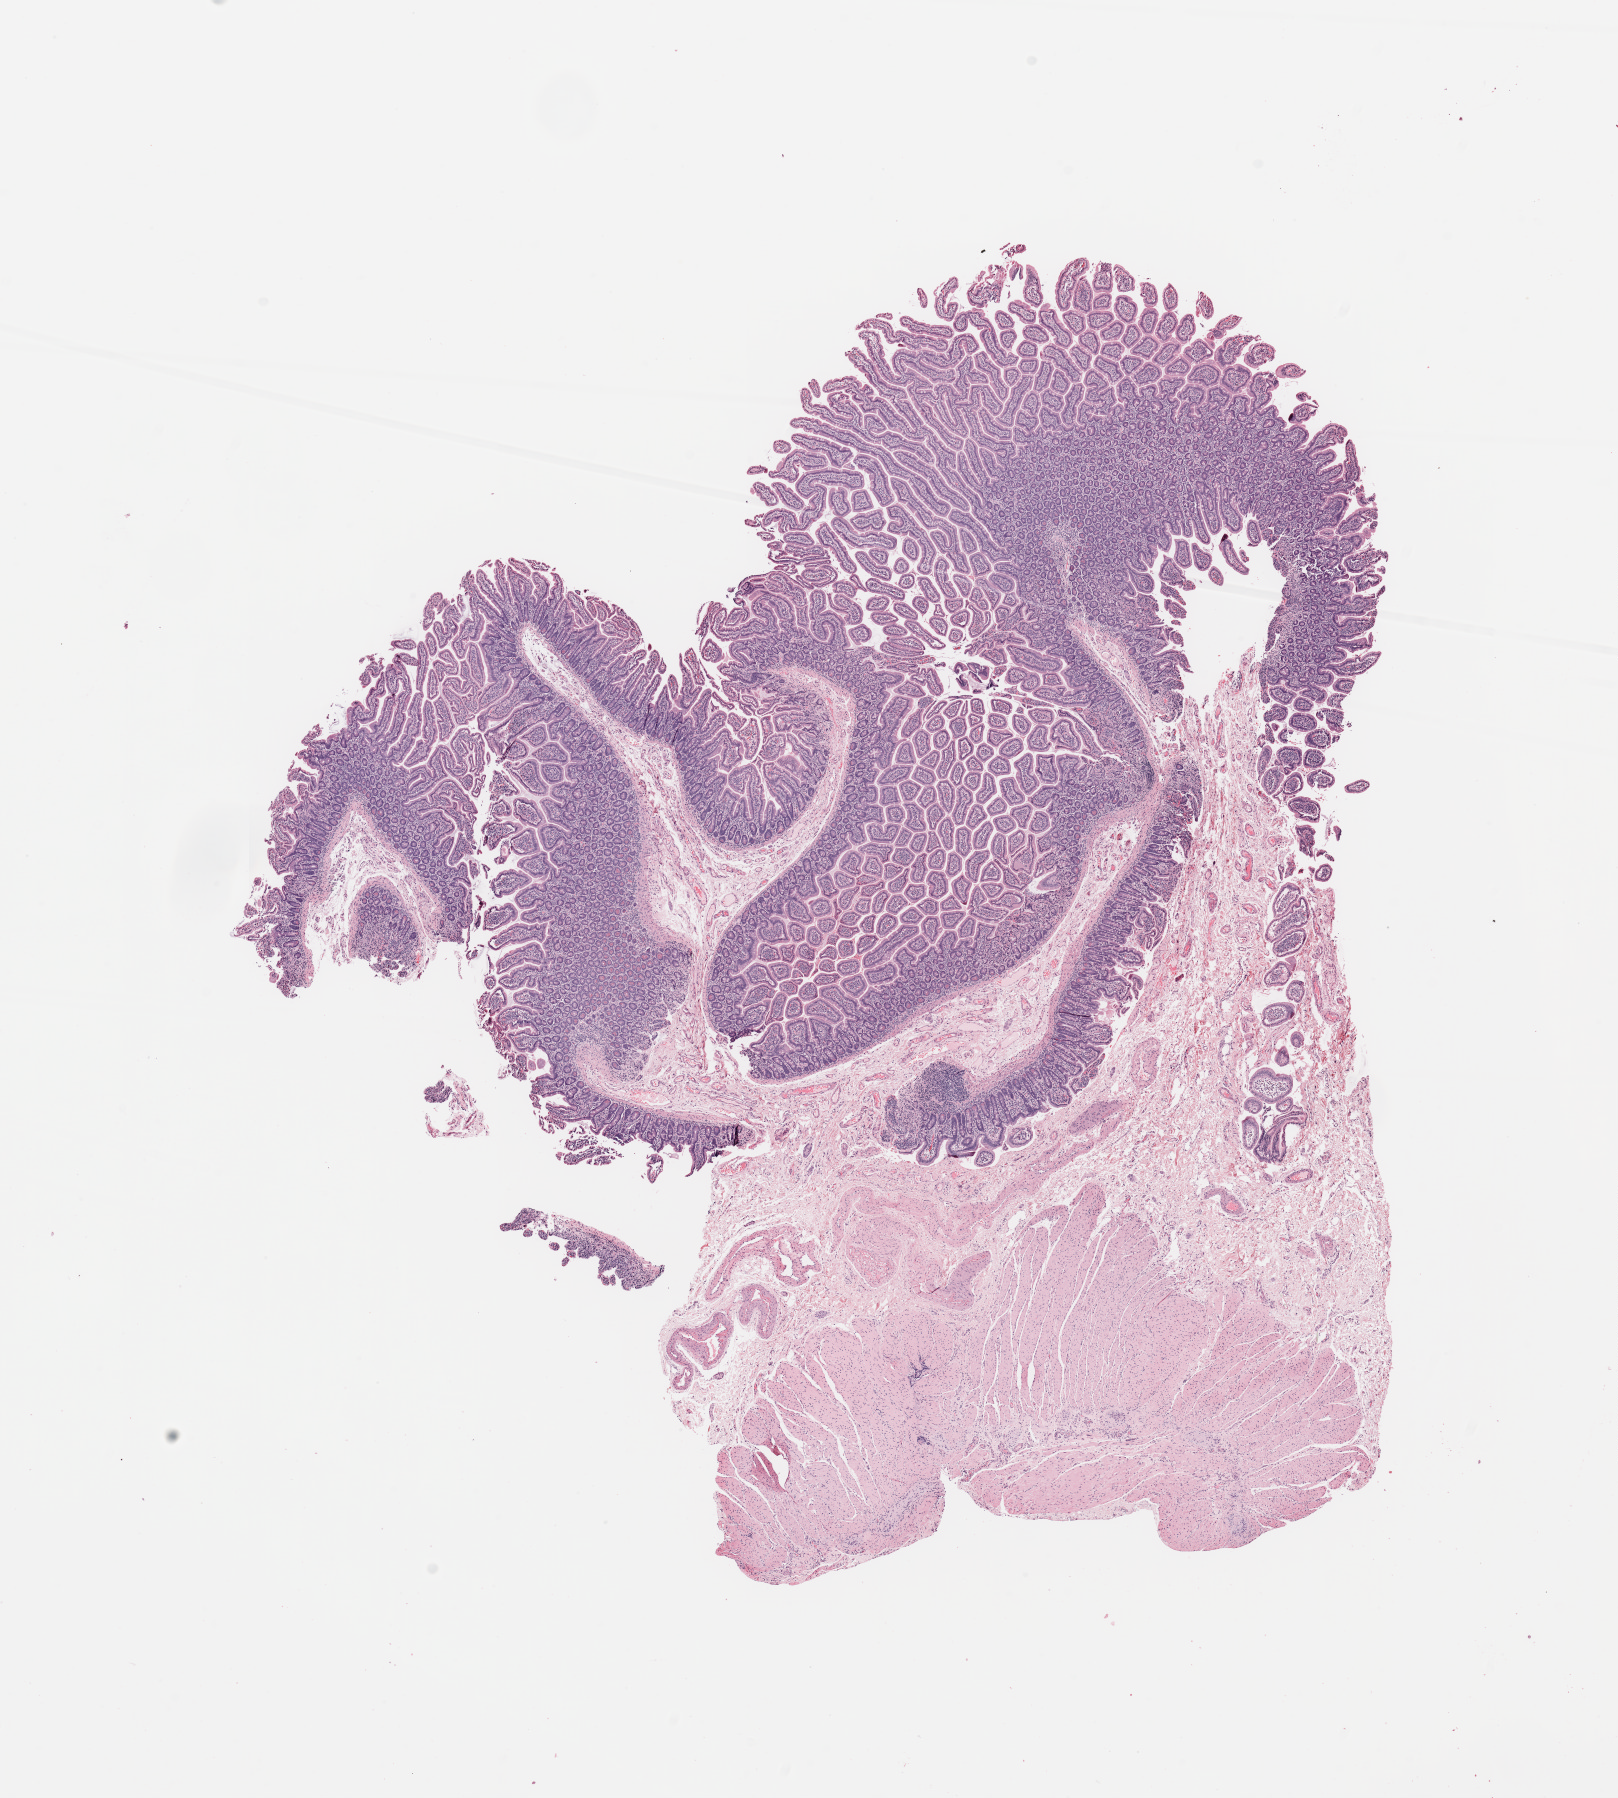
Digitized H&E tissue section (whole slide), whole scanned area (about 12.8 x 14.2 mm, slide scanned at 20x) shown as a low-resolution overview. Normal (non-tumour) tissue sample, sampled site: pancreas. 73-year-old female patient.
* this section: normal (non-tumour) tissue from the same patient
* patient diagnosis: Infiltrating duct carcinoma, NOS